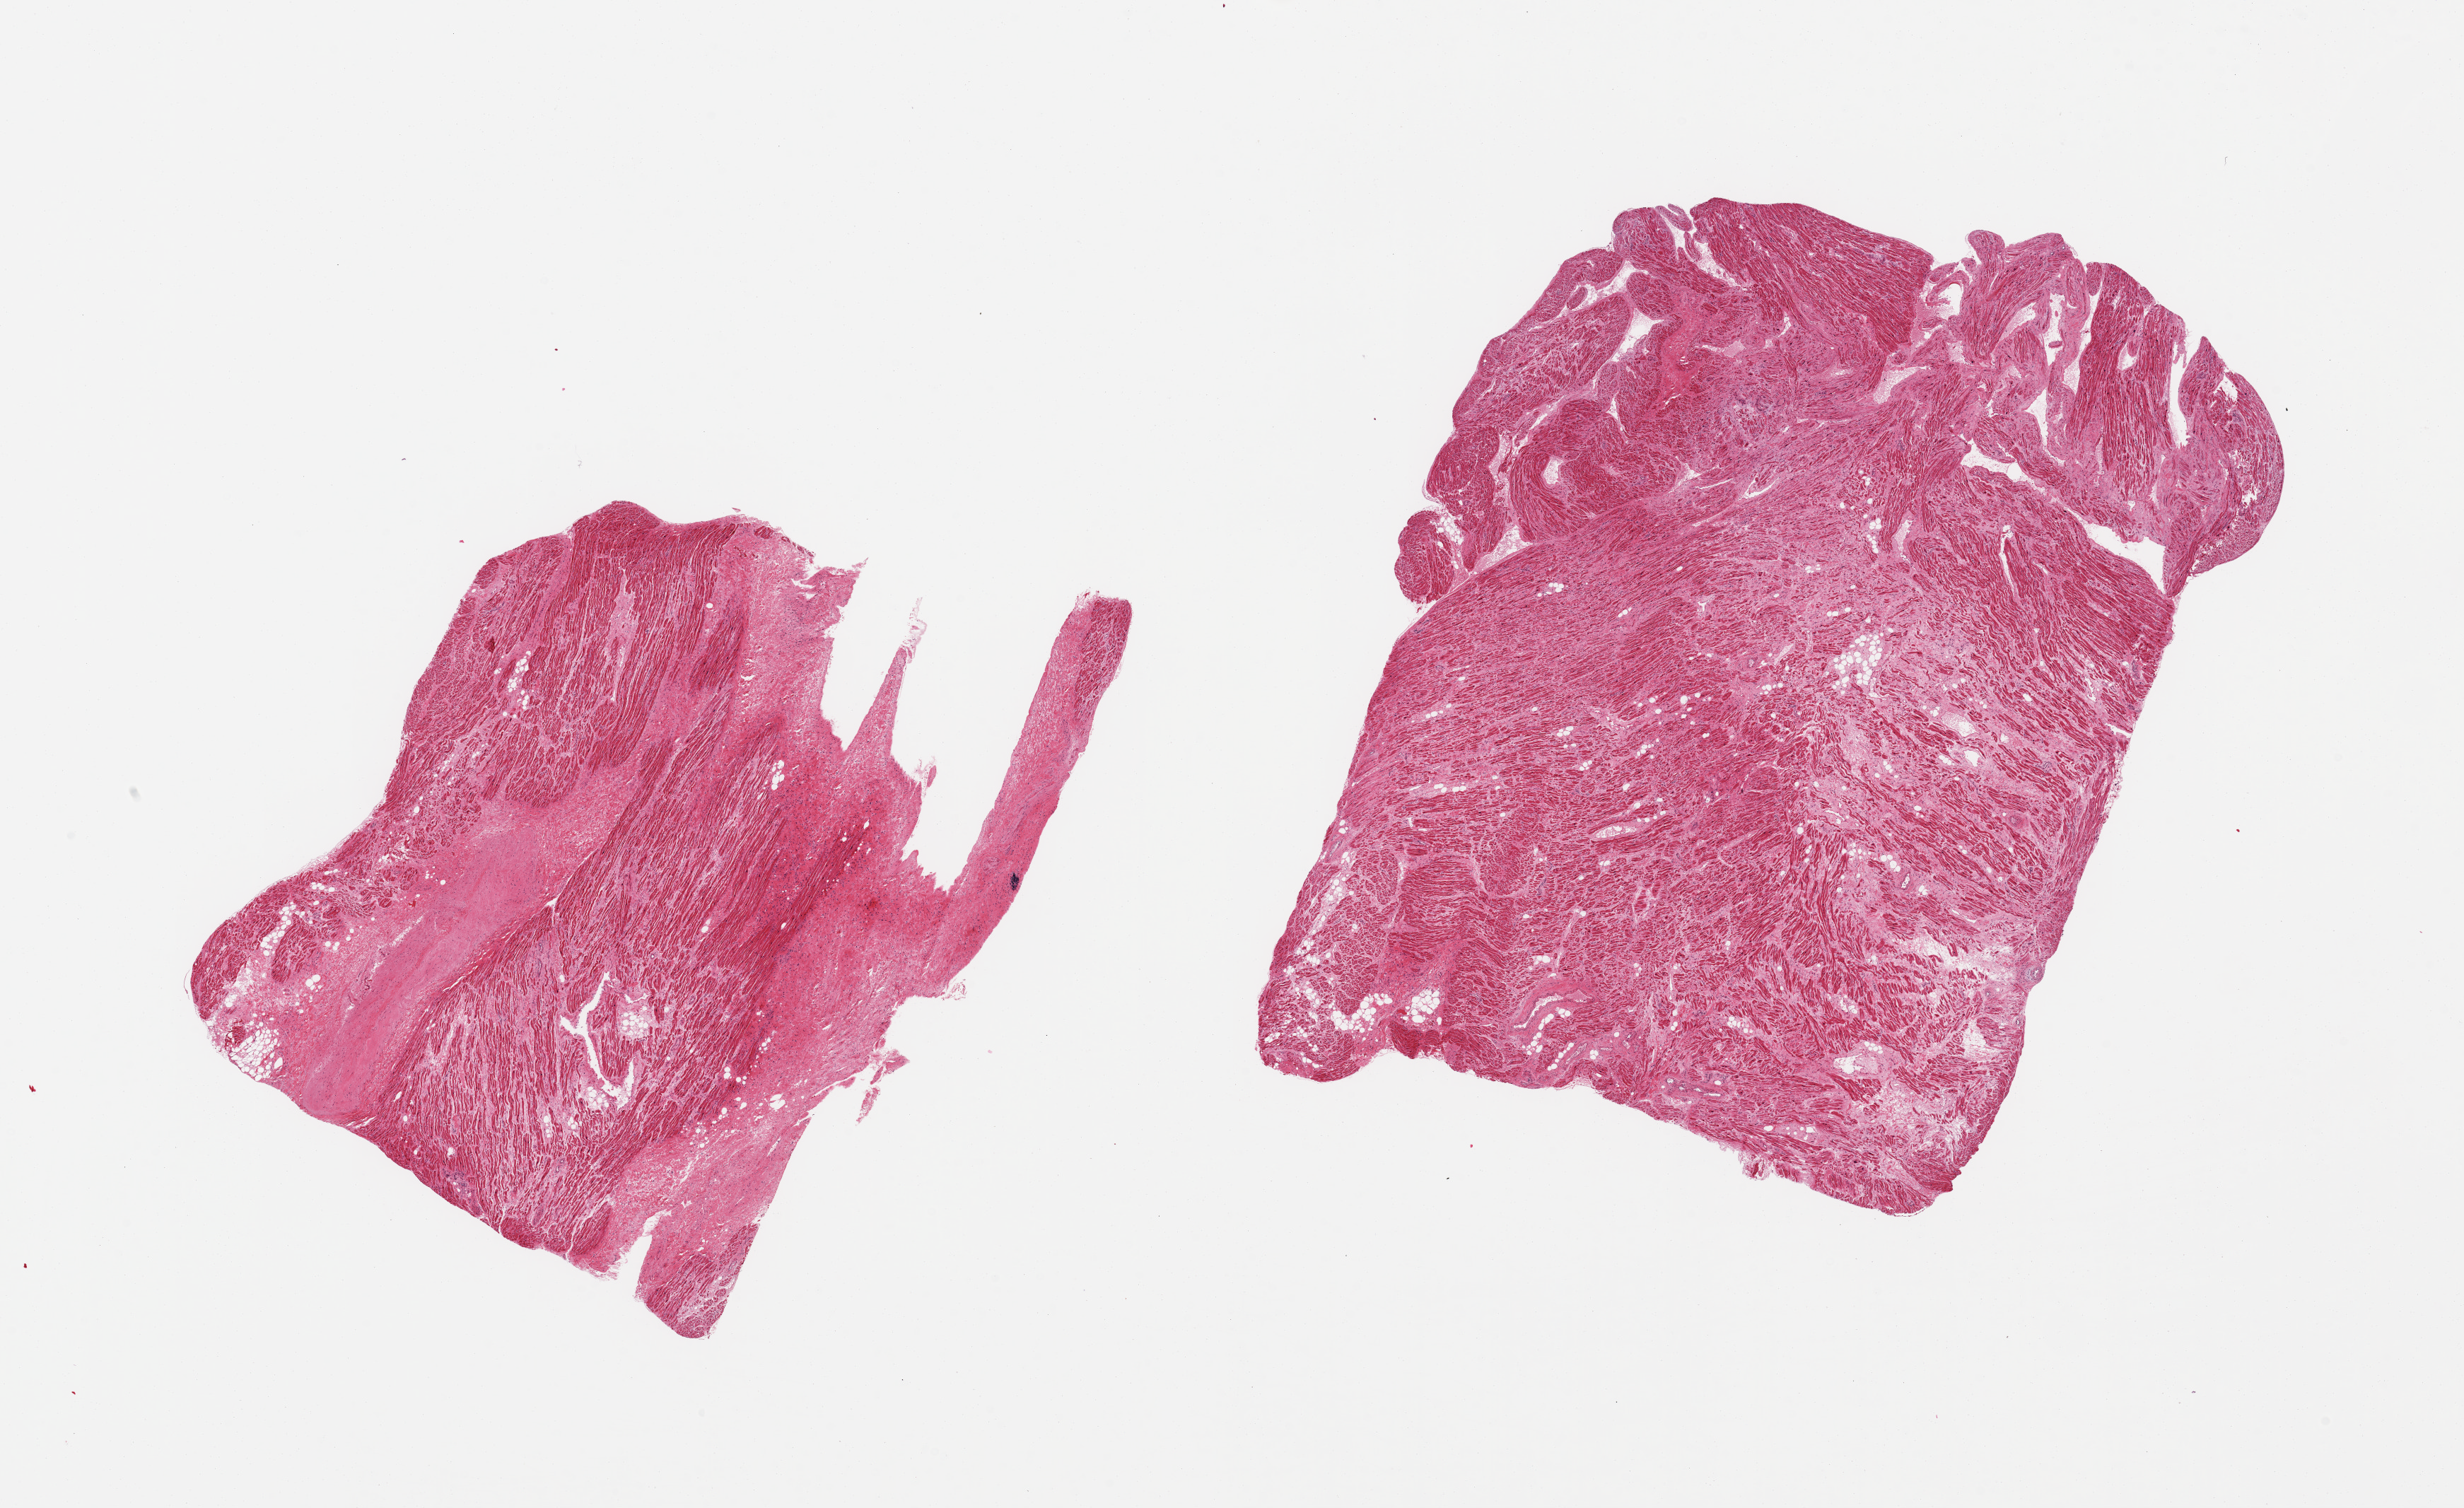
Digitized haematoxylin and eosin-stained section — a low-resolution overview of the entire scanned area, about 27.6 x 16.9 mm (slide scanned at 20x), PAXgene-fixed, paraffin-embedded tissue, sampled site (target tissue): auricular appendage, tissue donor sample. Donor: male.
- review note (as recorded): 2 pieces: 30% & 5% internal fibrous content